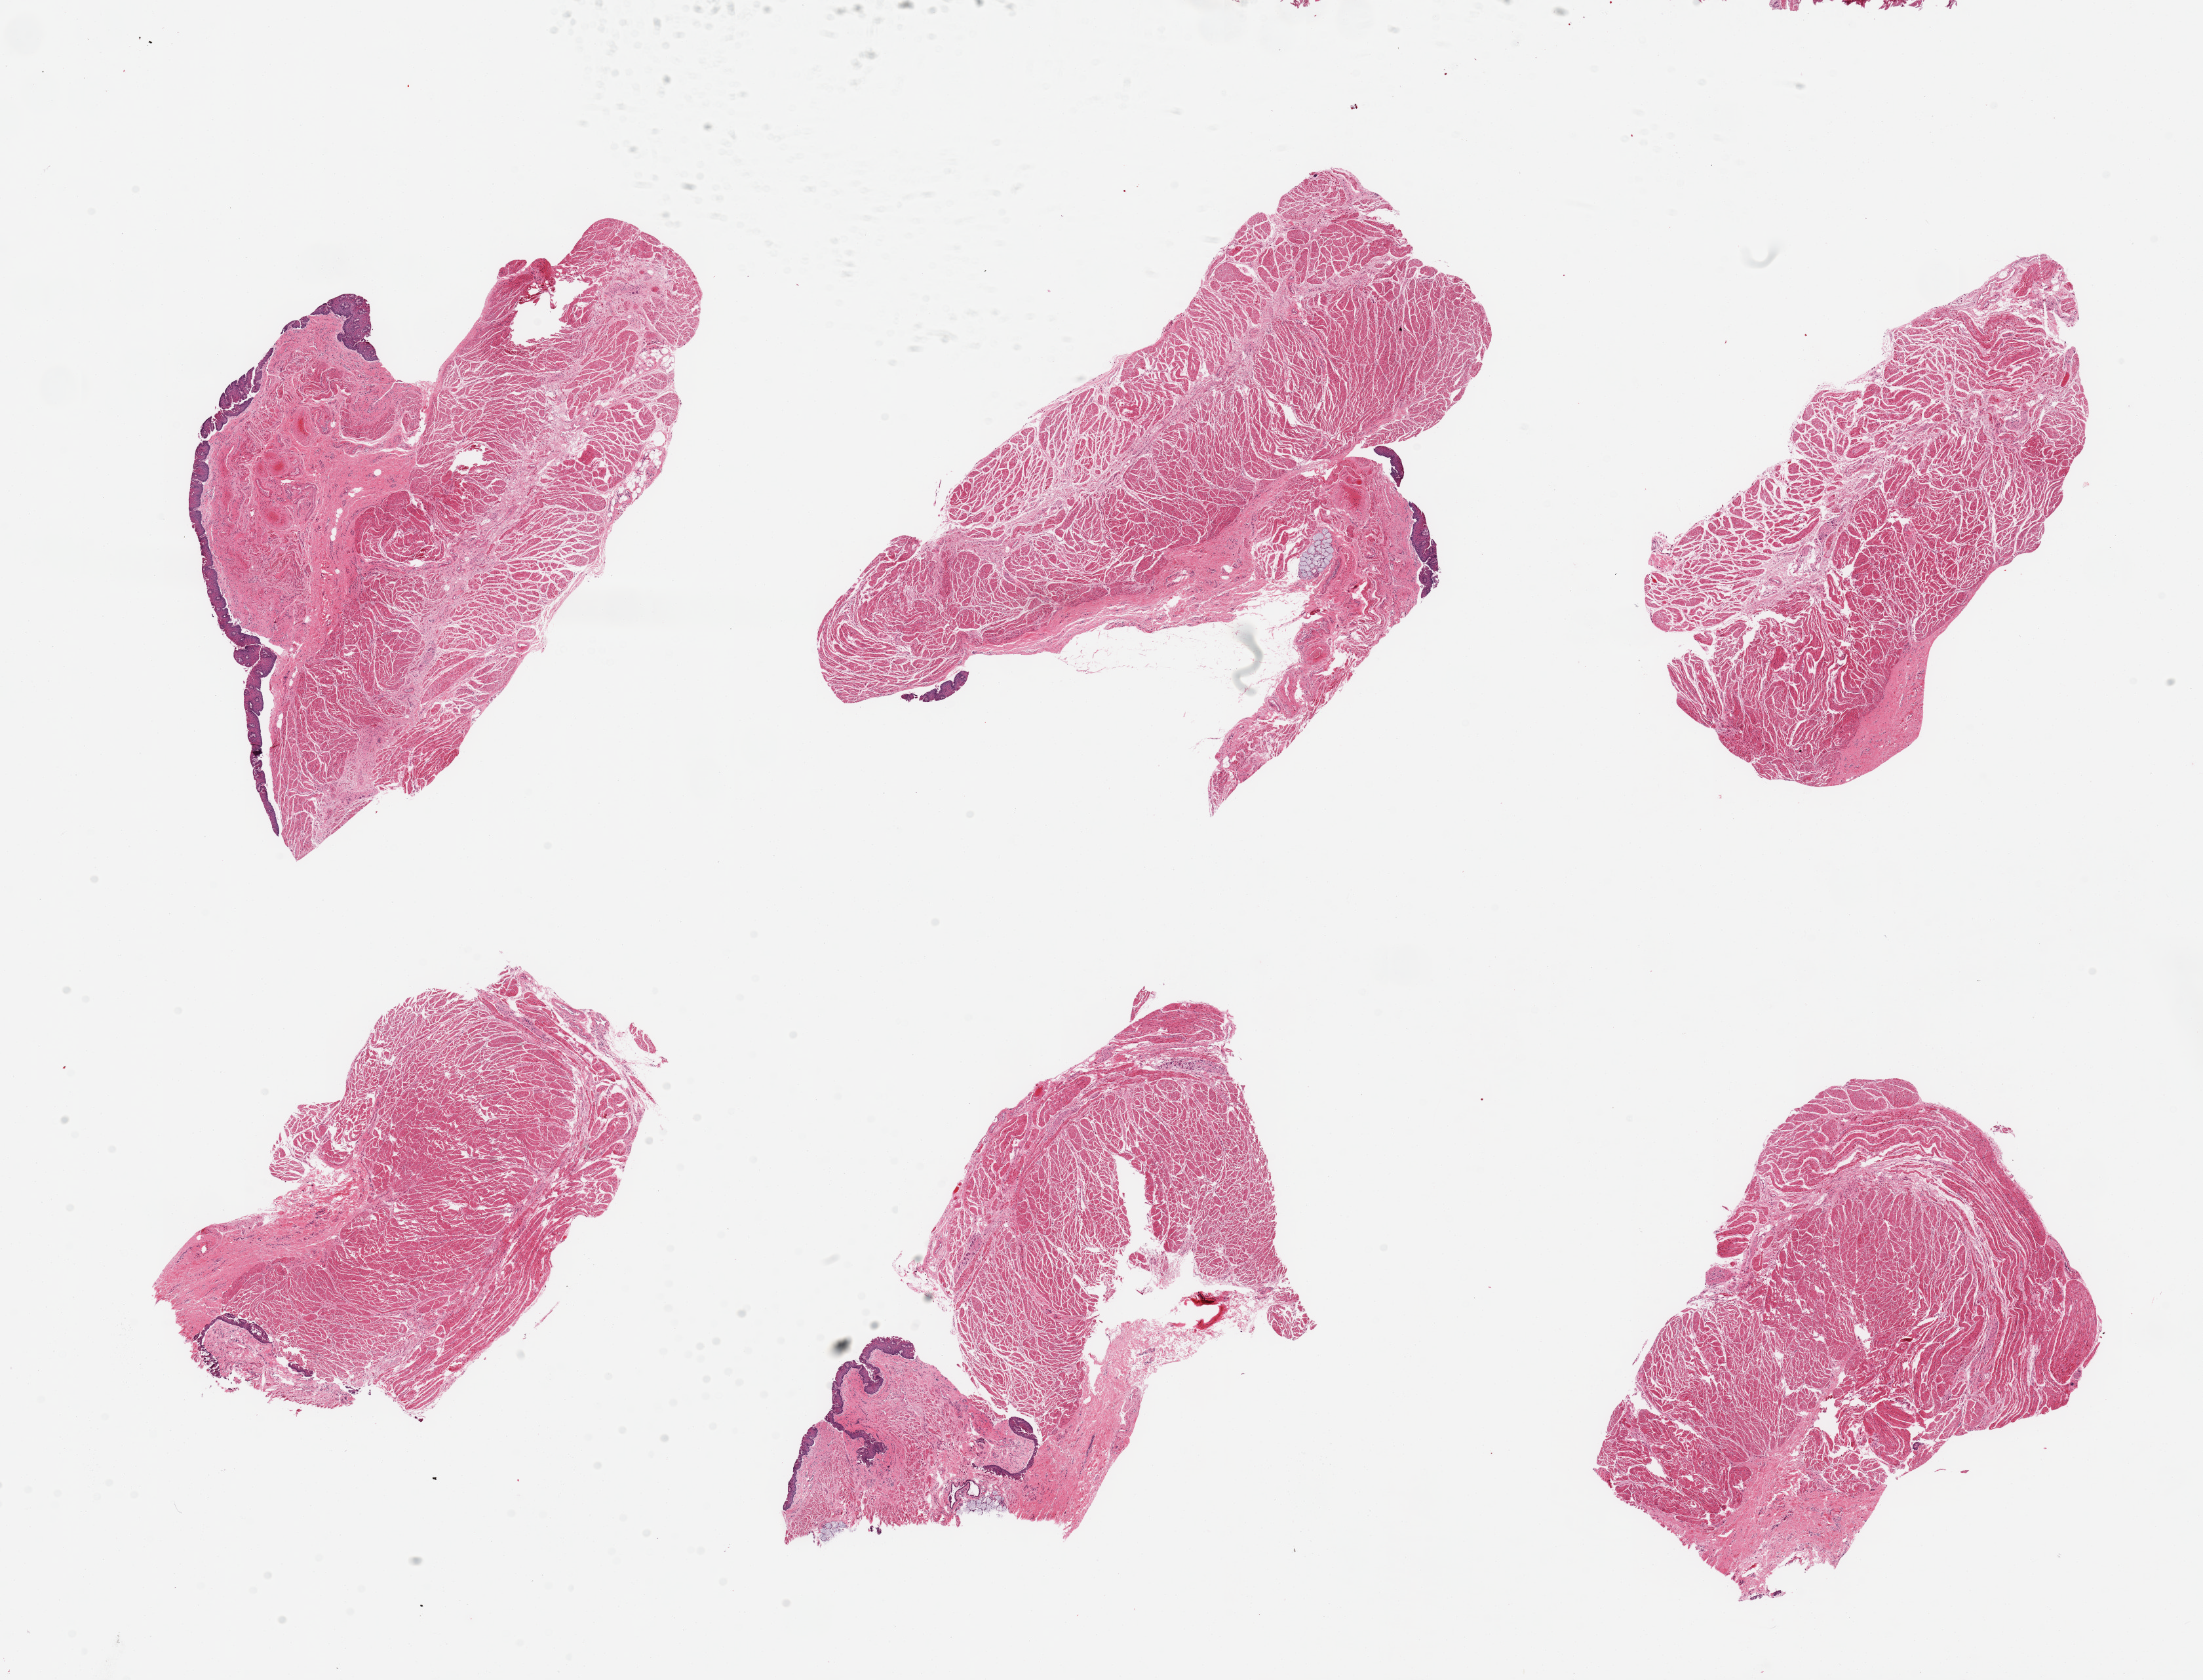
Whole-slide image, H&E stain, shown as a low-resolution overview of the whole scanned area (about 26.6 x 20.3 mm); PAXgene-fixed, paraffin-embedded tissue; sampled site (target tissue): gastroesophageal junction; donor tissue sample.
Reviewer comment on this tissue sample: 6 pieces, confirmed target muscularis; trace 'contaminant' squamous mucosa.